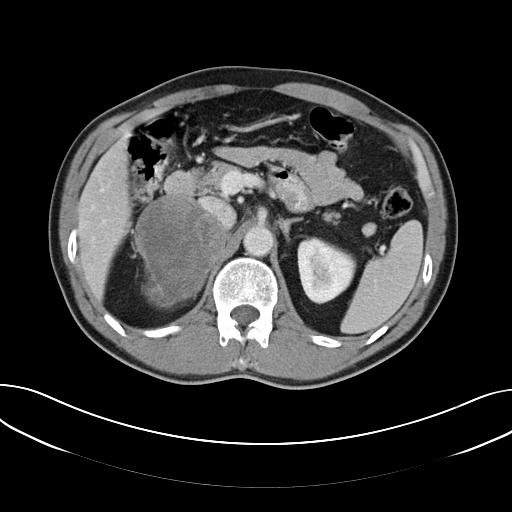
Contrast-enhanced abdominal CT, one axial slice; position 34 of 61 along the scan axis; reconstruction kernel B40f; intravenous contrast given; soft-tissue window (W 400 / L 40 HU); 5 mm slice thickness; 512 × 512 image matrix, field of view 372 × 372 mm. Male patient, age 57 years. From the clinical record (not read from this slice): diagnosis: adrenocortical carcinoma; tumour side: right adrenal; tumour size at pathology: 11.2 cm; Ki-67 index: 10 %; stage (as recorded): 3.
Outlined on this slice (semi-automatic segmentation, software-assisted and operator-edited):
- mass: bounding box (x1, y1, x2, y2) in pixels: (135, 196, 224, 307)